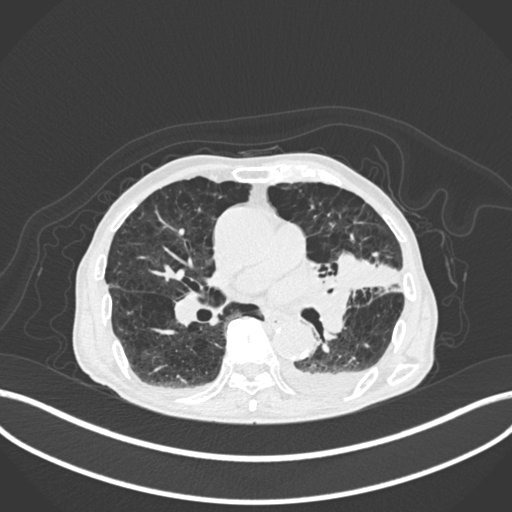
Chest CT, one axial slice; lung window (W 1500 / L -600 HU); 1 mm slice thickness; 512 × 512 image matrix, field of view 400 × 400 mm. Male patient, age 90 years or older. From the clinical record (not read from this slice): clinical TNM (as recorded): T2b N1 M0.
Outlined on this slice (rectangle marked by the reading radiologist):
- lung tumour (recorded histology: squamous cell carcinoma): bounding box [x1, y1, x2, y2] px = [326, 246, 404, 300]